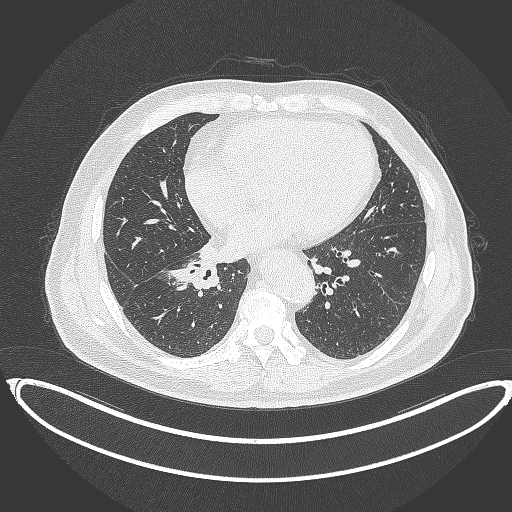
Chest CT, one axial slice. Lung window (W 1500 / L -600 HU). 512 × 512 image matrix, field of view 448 × 448 mm. Patient: male, 61 years. Case-level facts recorded for this patient, not image findings: clinical TNM (as recorded): T1b N1 M0.
Outlined on this slice (rectangle marked by the reading radiologist):
- lung tumour (recorded histology: squamous cell carcinoma): bounding box [x1, y1, x2, y2] px = [165, 252, 224, 290]